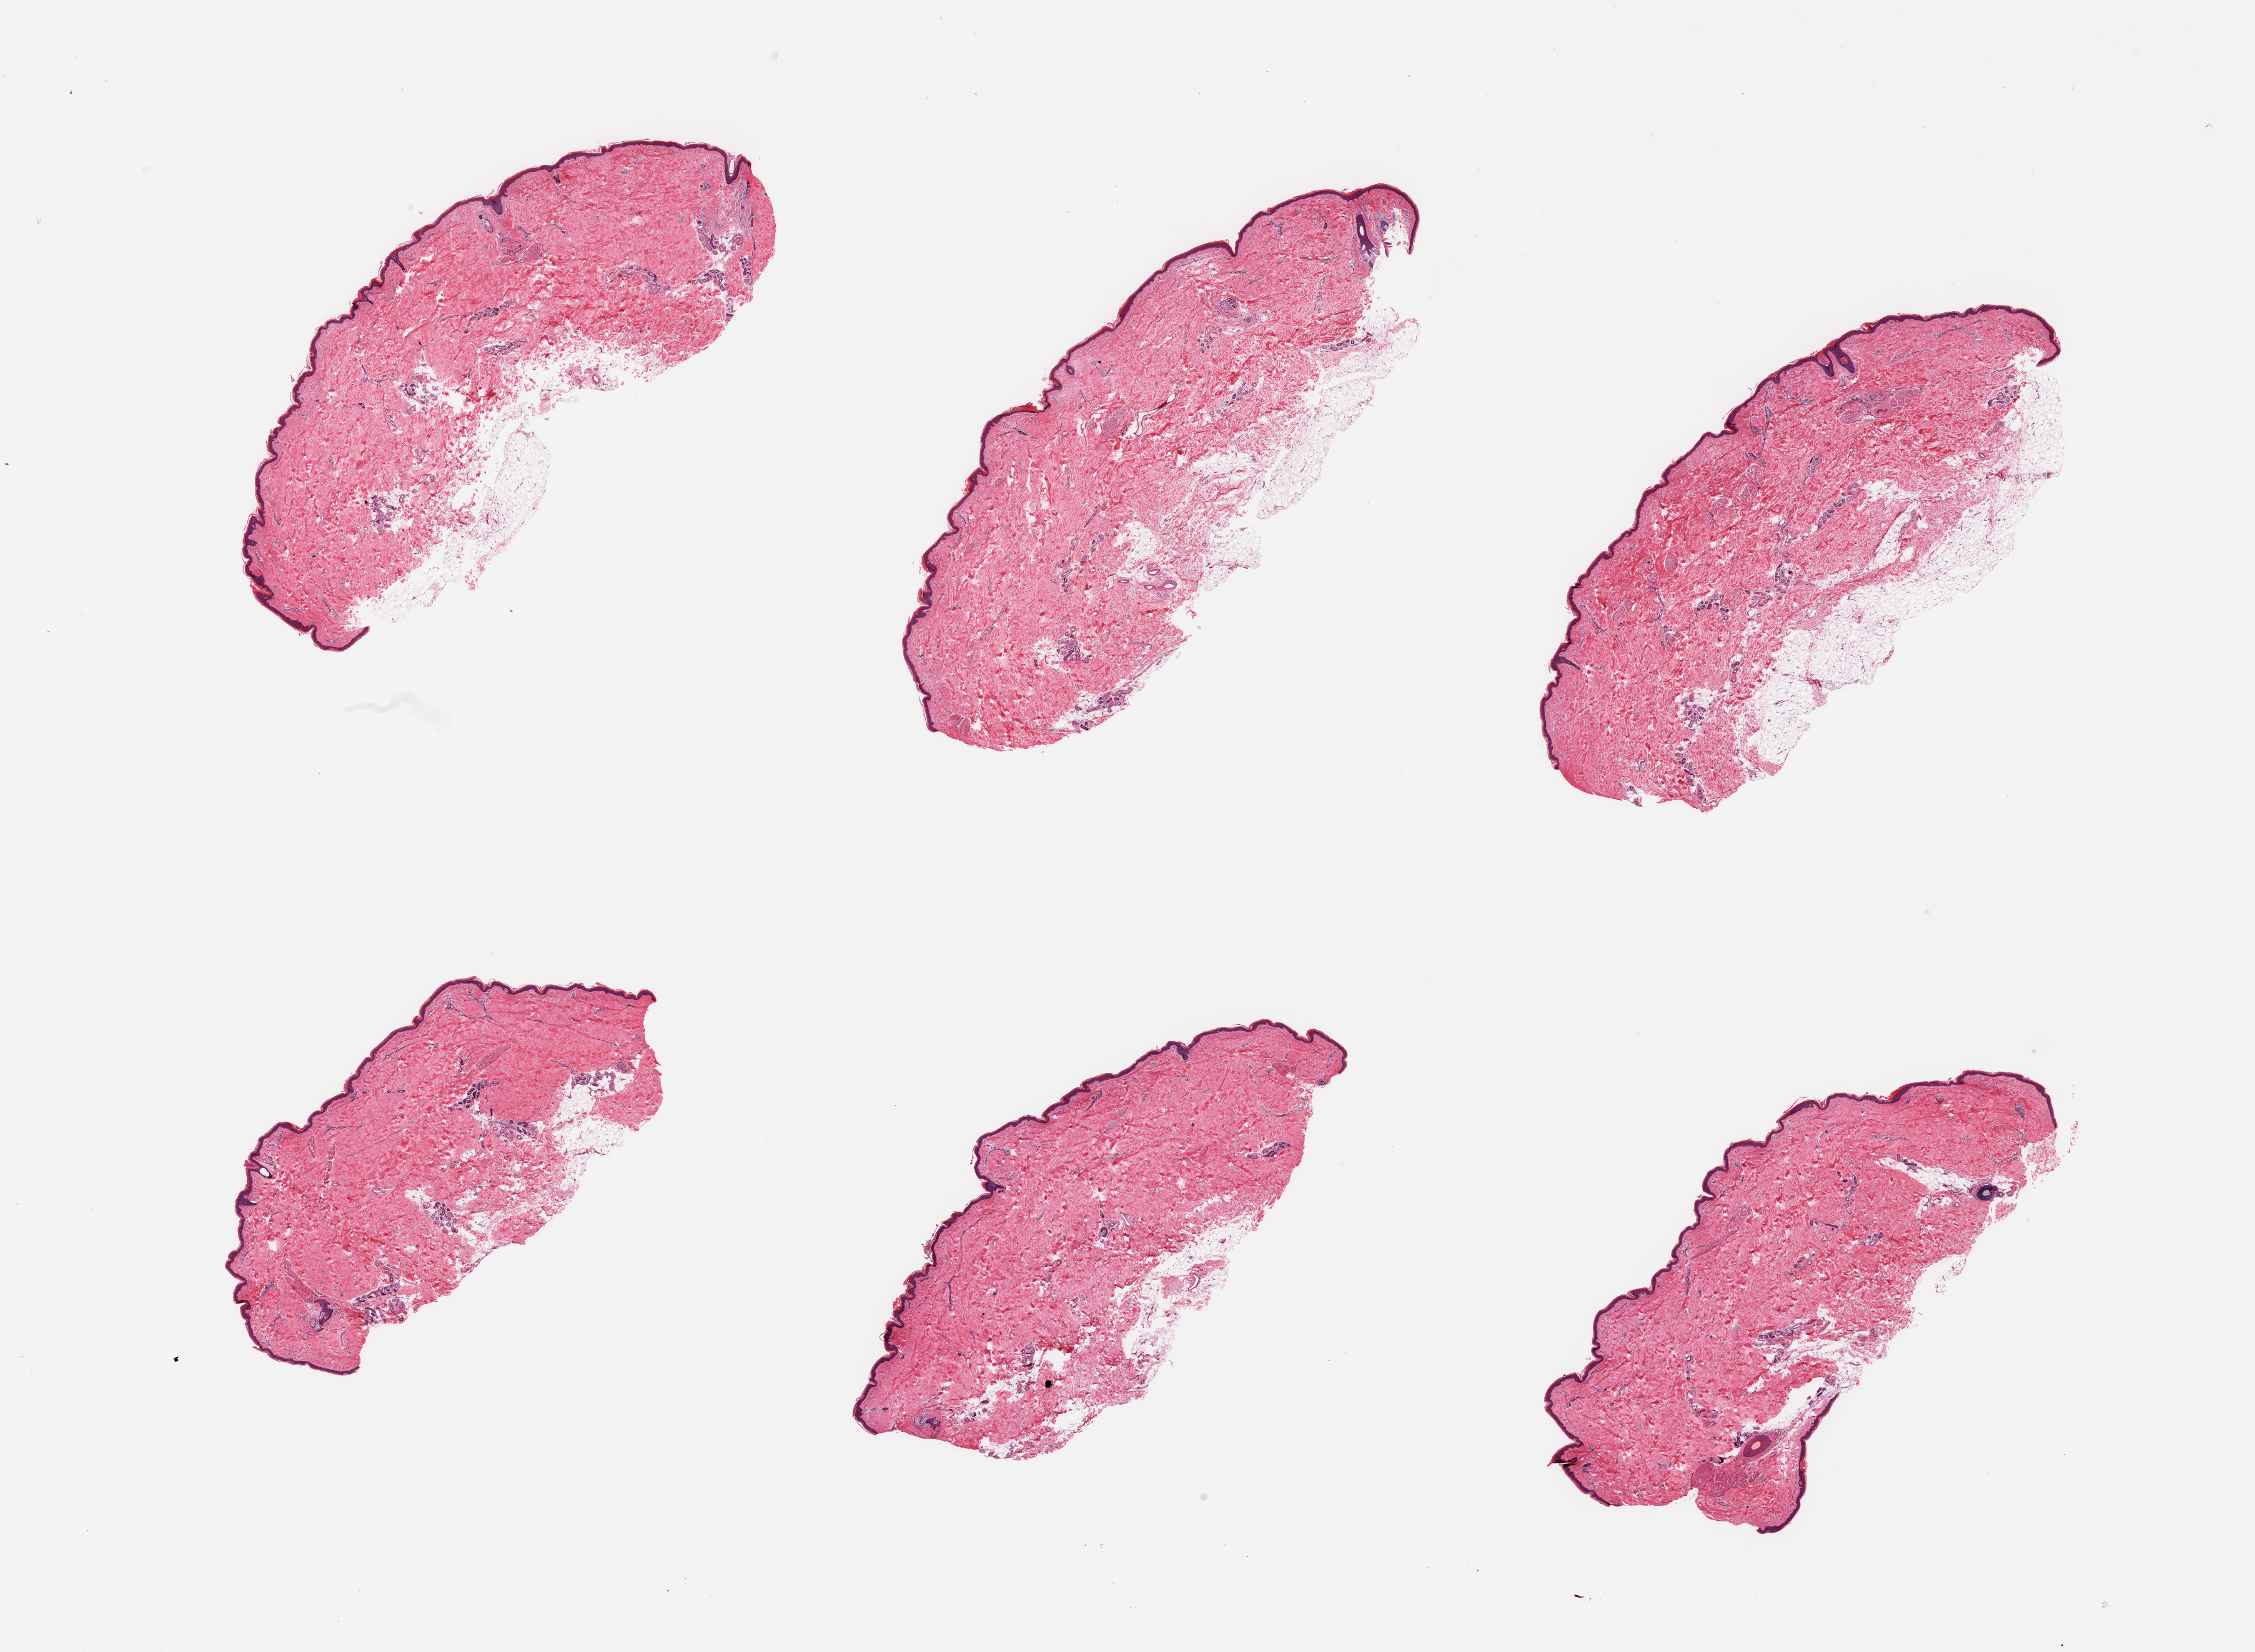
Whole-slide image, haematoxylin and eosin stain, shown as a low-resolution overview of the whole scanned area (about 28.5 x 20.9 mm, slide scanned at 20x). PAXgene-fixed, paraffin-embedded tissue. Section of skin of lower leg (target tissue). Tissue donor sample. Donor sex: male.
Review note (as recorded): 6 pieces, adherent fat nubbins up to ~4mm; squamous epithelium is ~40-50 microns.